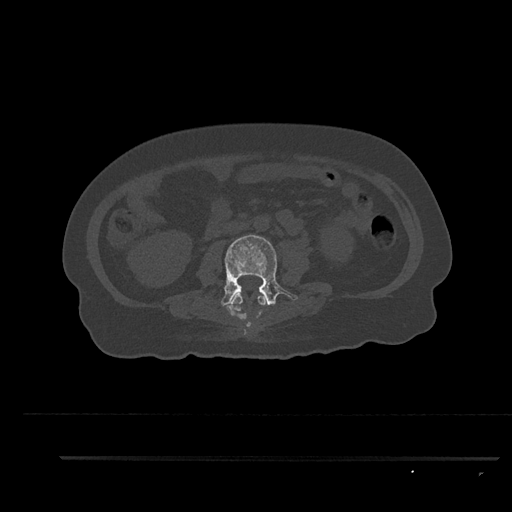
CT including the spine, one axial slice. Position 105 of 797 along the scan axis. Bone window (W 1800 / L 400 HU). 0.5 mm slice thickness. 512 × 512 image matrix, field of view 408 × 408 mm. Female patient, age 44 years. From the clinical record (not read from this slice): primary cancer: renal.
Annotated regions visible in this slice (semi-automatically segmented with operator editing):
- L2 vertebra: bounding box <231,293,266,328> (left, top, right, bottom; pixels)
- L3 vertebra: <221,234,298,316>